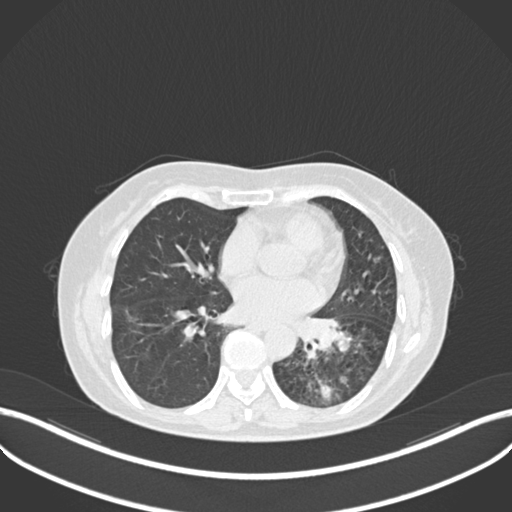
Chest CT, one axial slice. Position 115 of 270 along the scan axis. 120 kVp. Lung window (W 1500 / L -600 HU). 1 mm slice thickness. 512 × 512 image matrix, field of view 400 × 400 mm. Female patient, age 63 years. Case-level facts recorded for this patient, not image findings: clinical TNM (as recorded): T1b N0 M0; histopathological grade: G2-3.
Structures marked on this image (rectangle marked by the reading radiologist):
- lung tumour (recorded histology: adenocarcinoma): bounding box (x1, y1, x2, y2) in pixels: (295, 312, 354, 360)